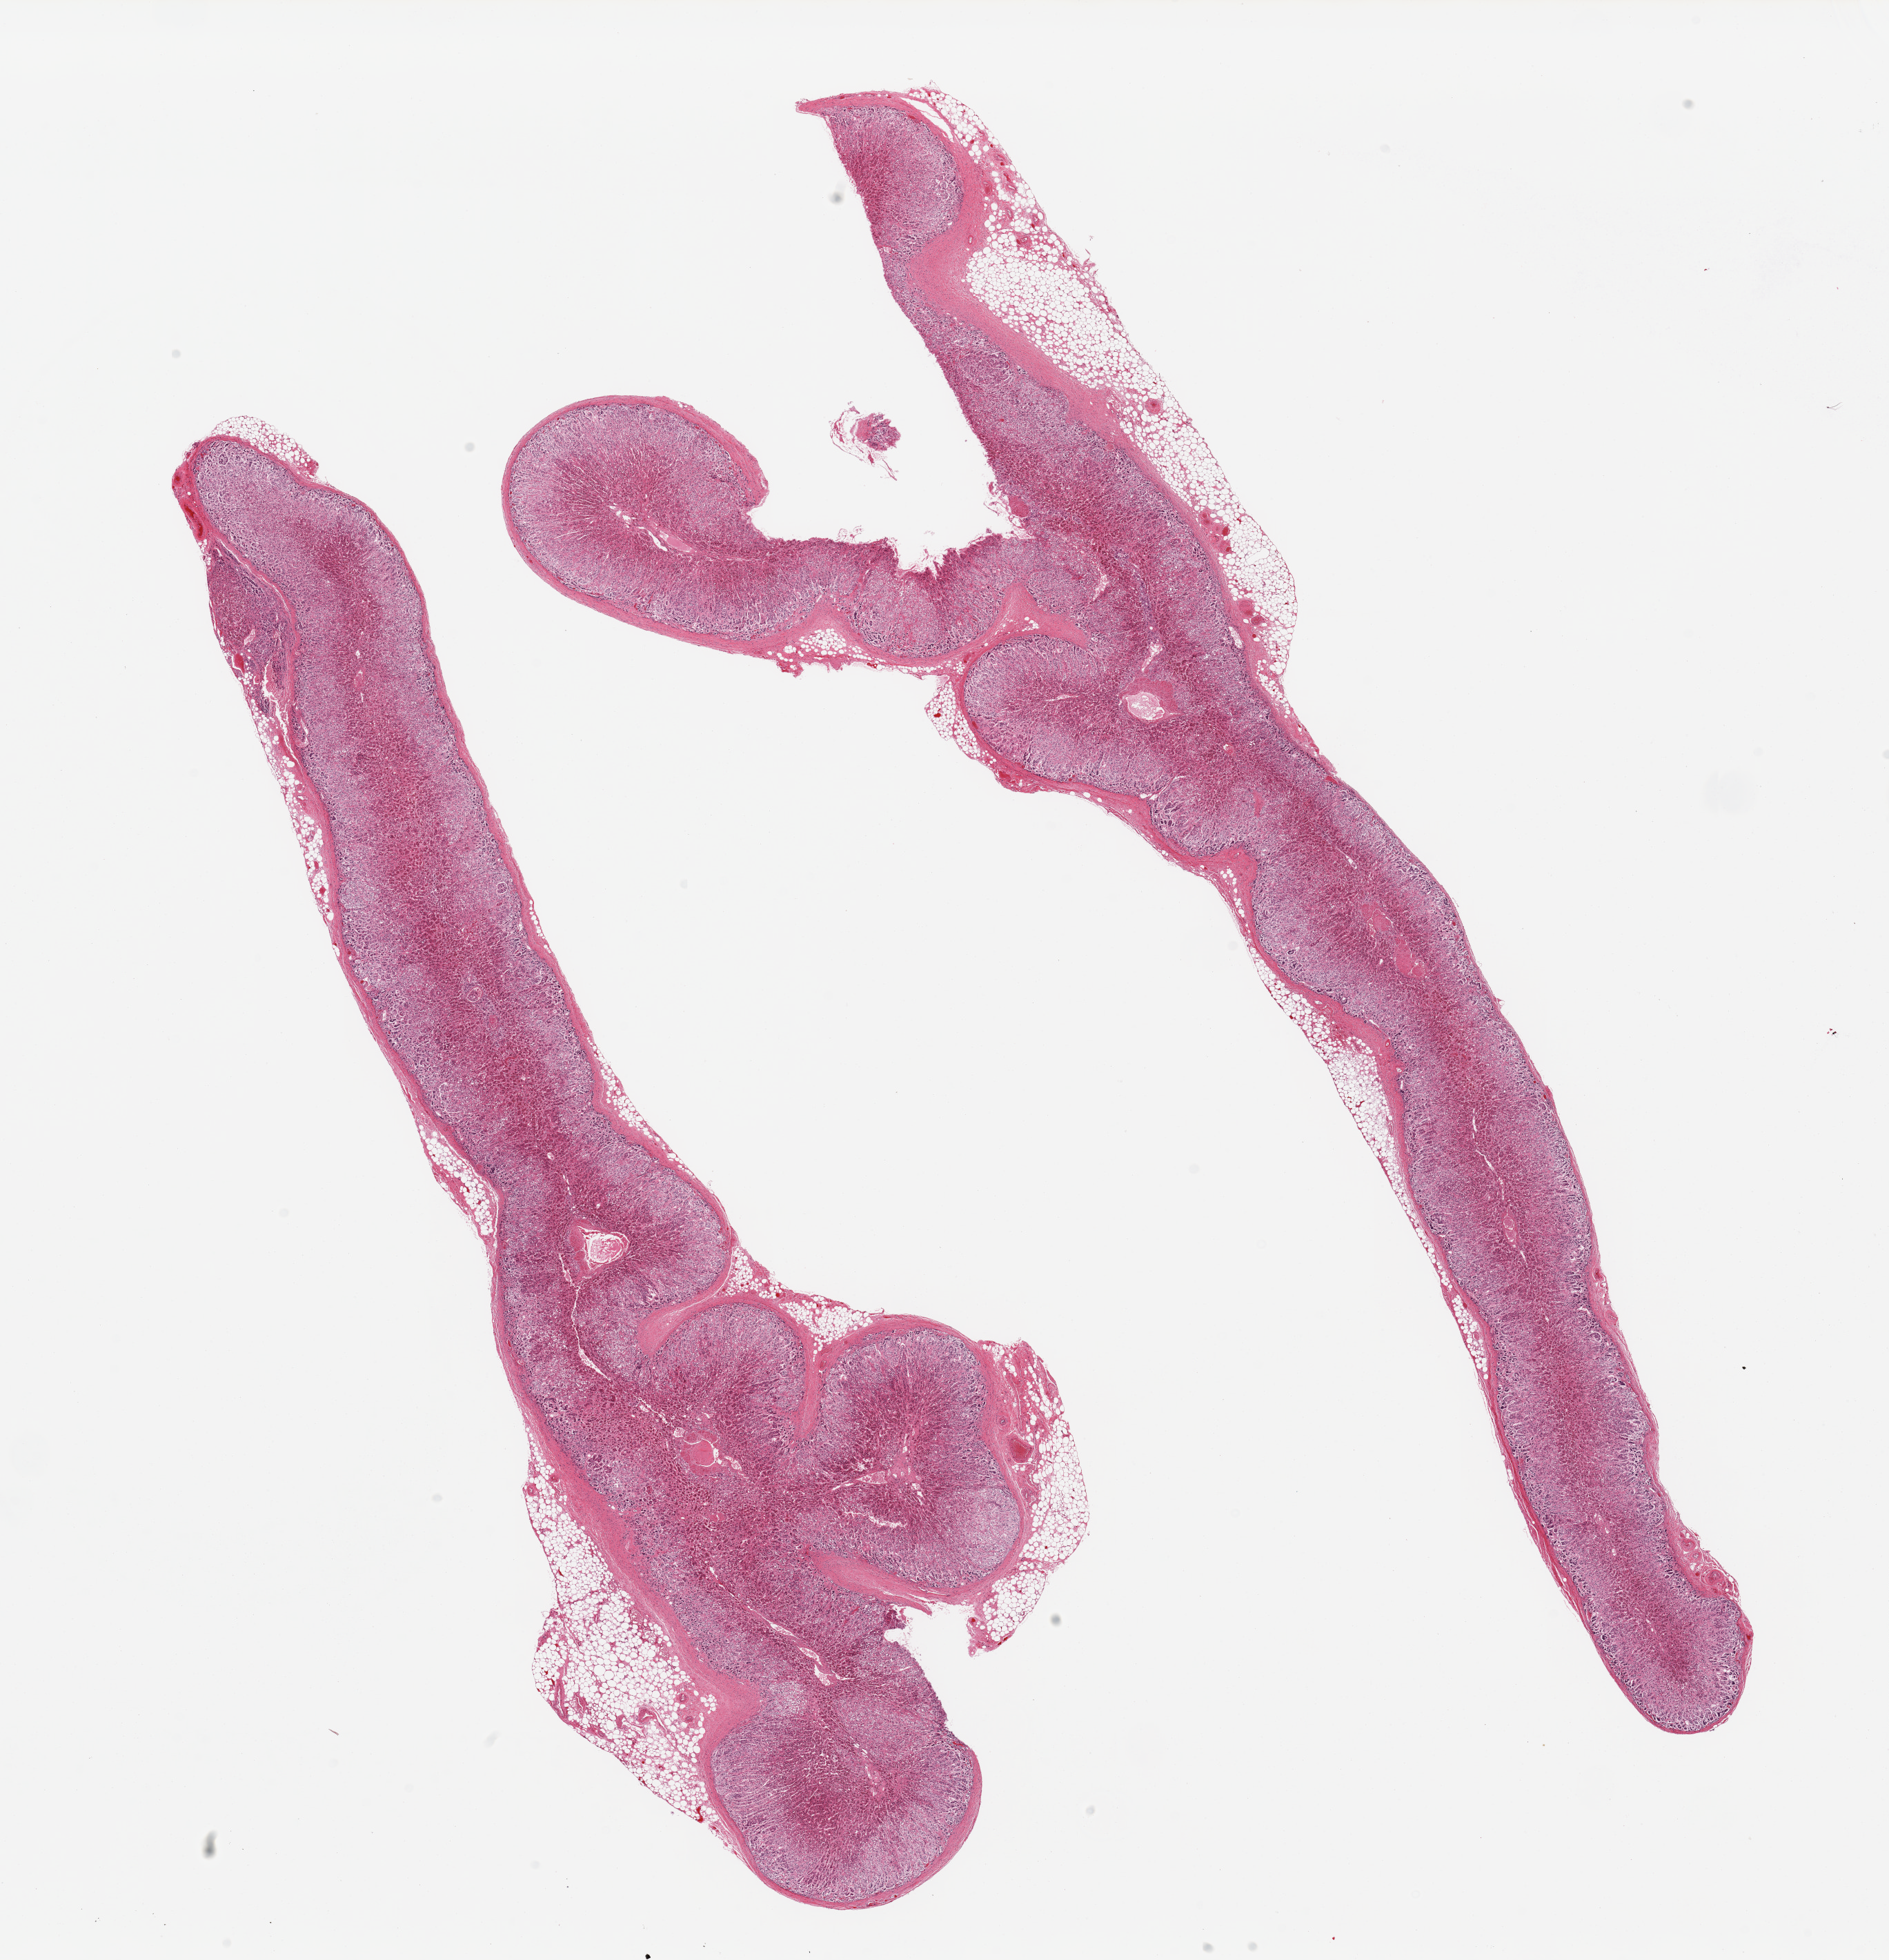
Whole-slide image, H&E stain, low-resolution overview of the scanned area, about 21.7 x 22.5 mm; PAXgene-fixed, paraffin-embedded tissue; target tissue: adrenal gland; donor tissue sample. Male donor.
* review note (as recorded): 2 pieces; some attached fat, from 5-10%